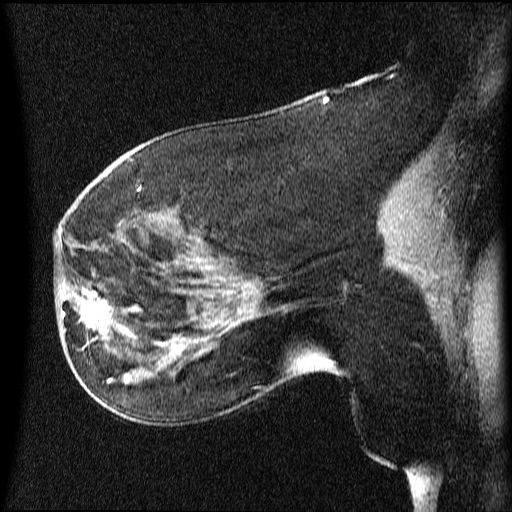
Breast MRI (dynamic contrast-enhanced), one sagittal slice. Position 31 of 64 along the scan axis. Dynamic contrast-enhanced series, image 2 of 4 at this slice position (ordered by acquisition). 1.5 T. TE 4.2 ms, TR 9 ms. 2 mm slice thickness. 512 × 512 image matrix, field of view 200 × 200 mm. Patient: female, 63 years.
Outlined on this slice (semi-automatic segmentation, software-assisted and operator-edited):
- analysis volume of interest (the breast-tissue region the enhancement analysis was run in; not a lesion): bounding box <66,272,131,353> (left, top, right, bottom; pixels)
- tumour enhancement mask (voxels above the 70 % enhancement threshold inside the analysis volume of interest): <77,290,131,337>